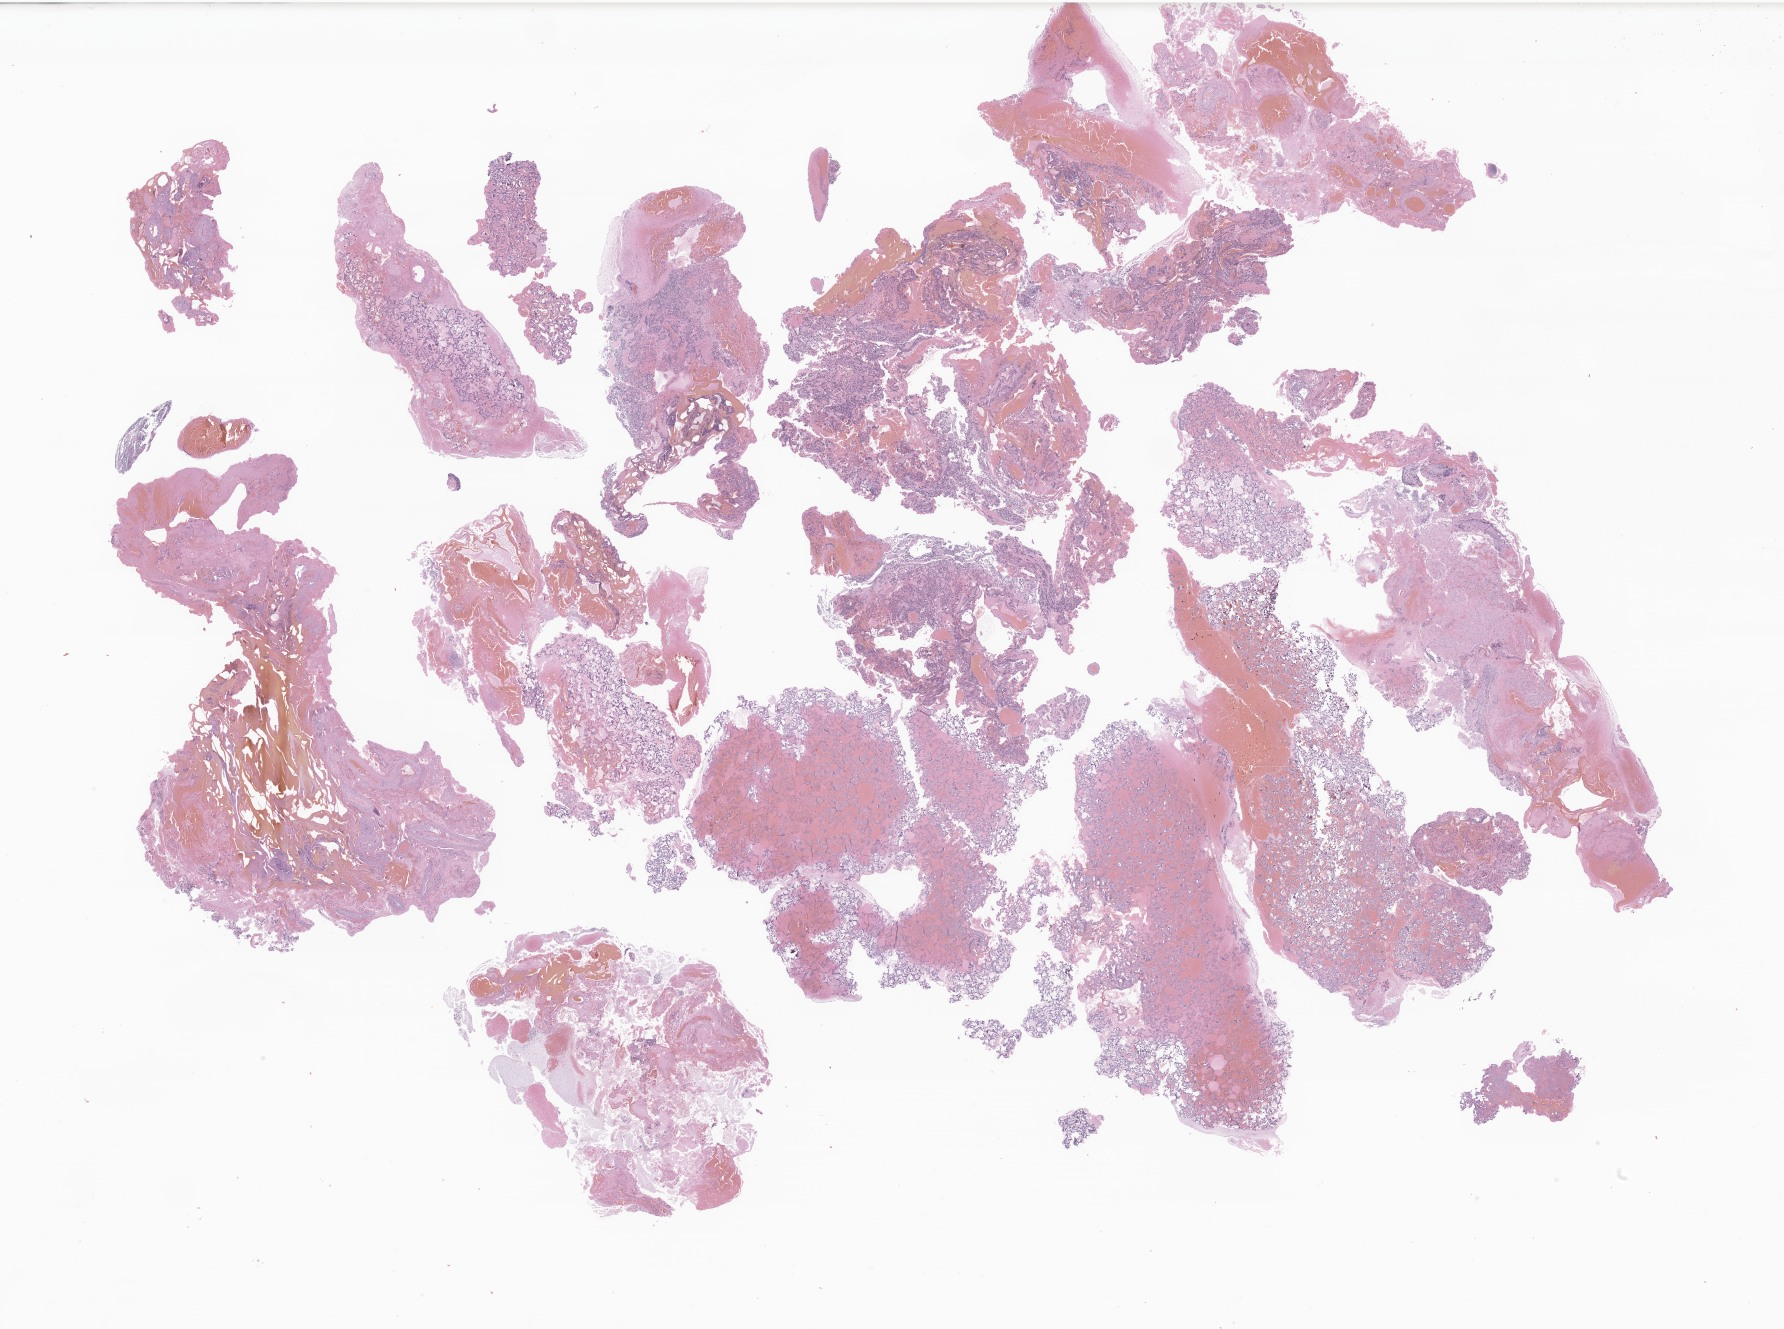
Whole-slide image, haematoxylin and eosin stain of tumor tissue from the brain — a low-resolution overview of the entire scanned area, about 30.1 x 22.4 mm; FFPE section. Female patient, age 198 months (16 years 6 months).
- diagnosis: Medulloblastoma, NOS